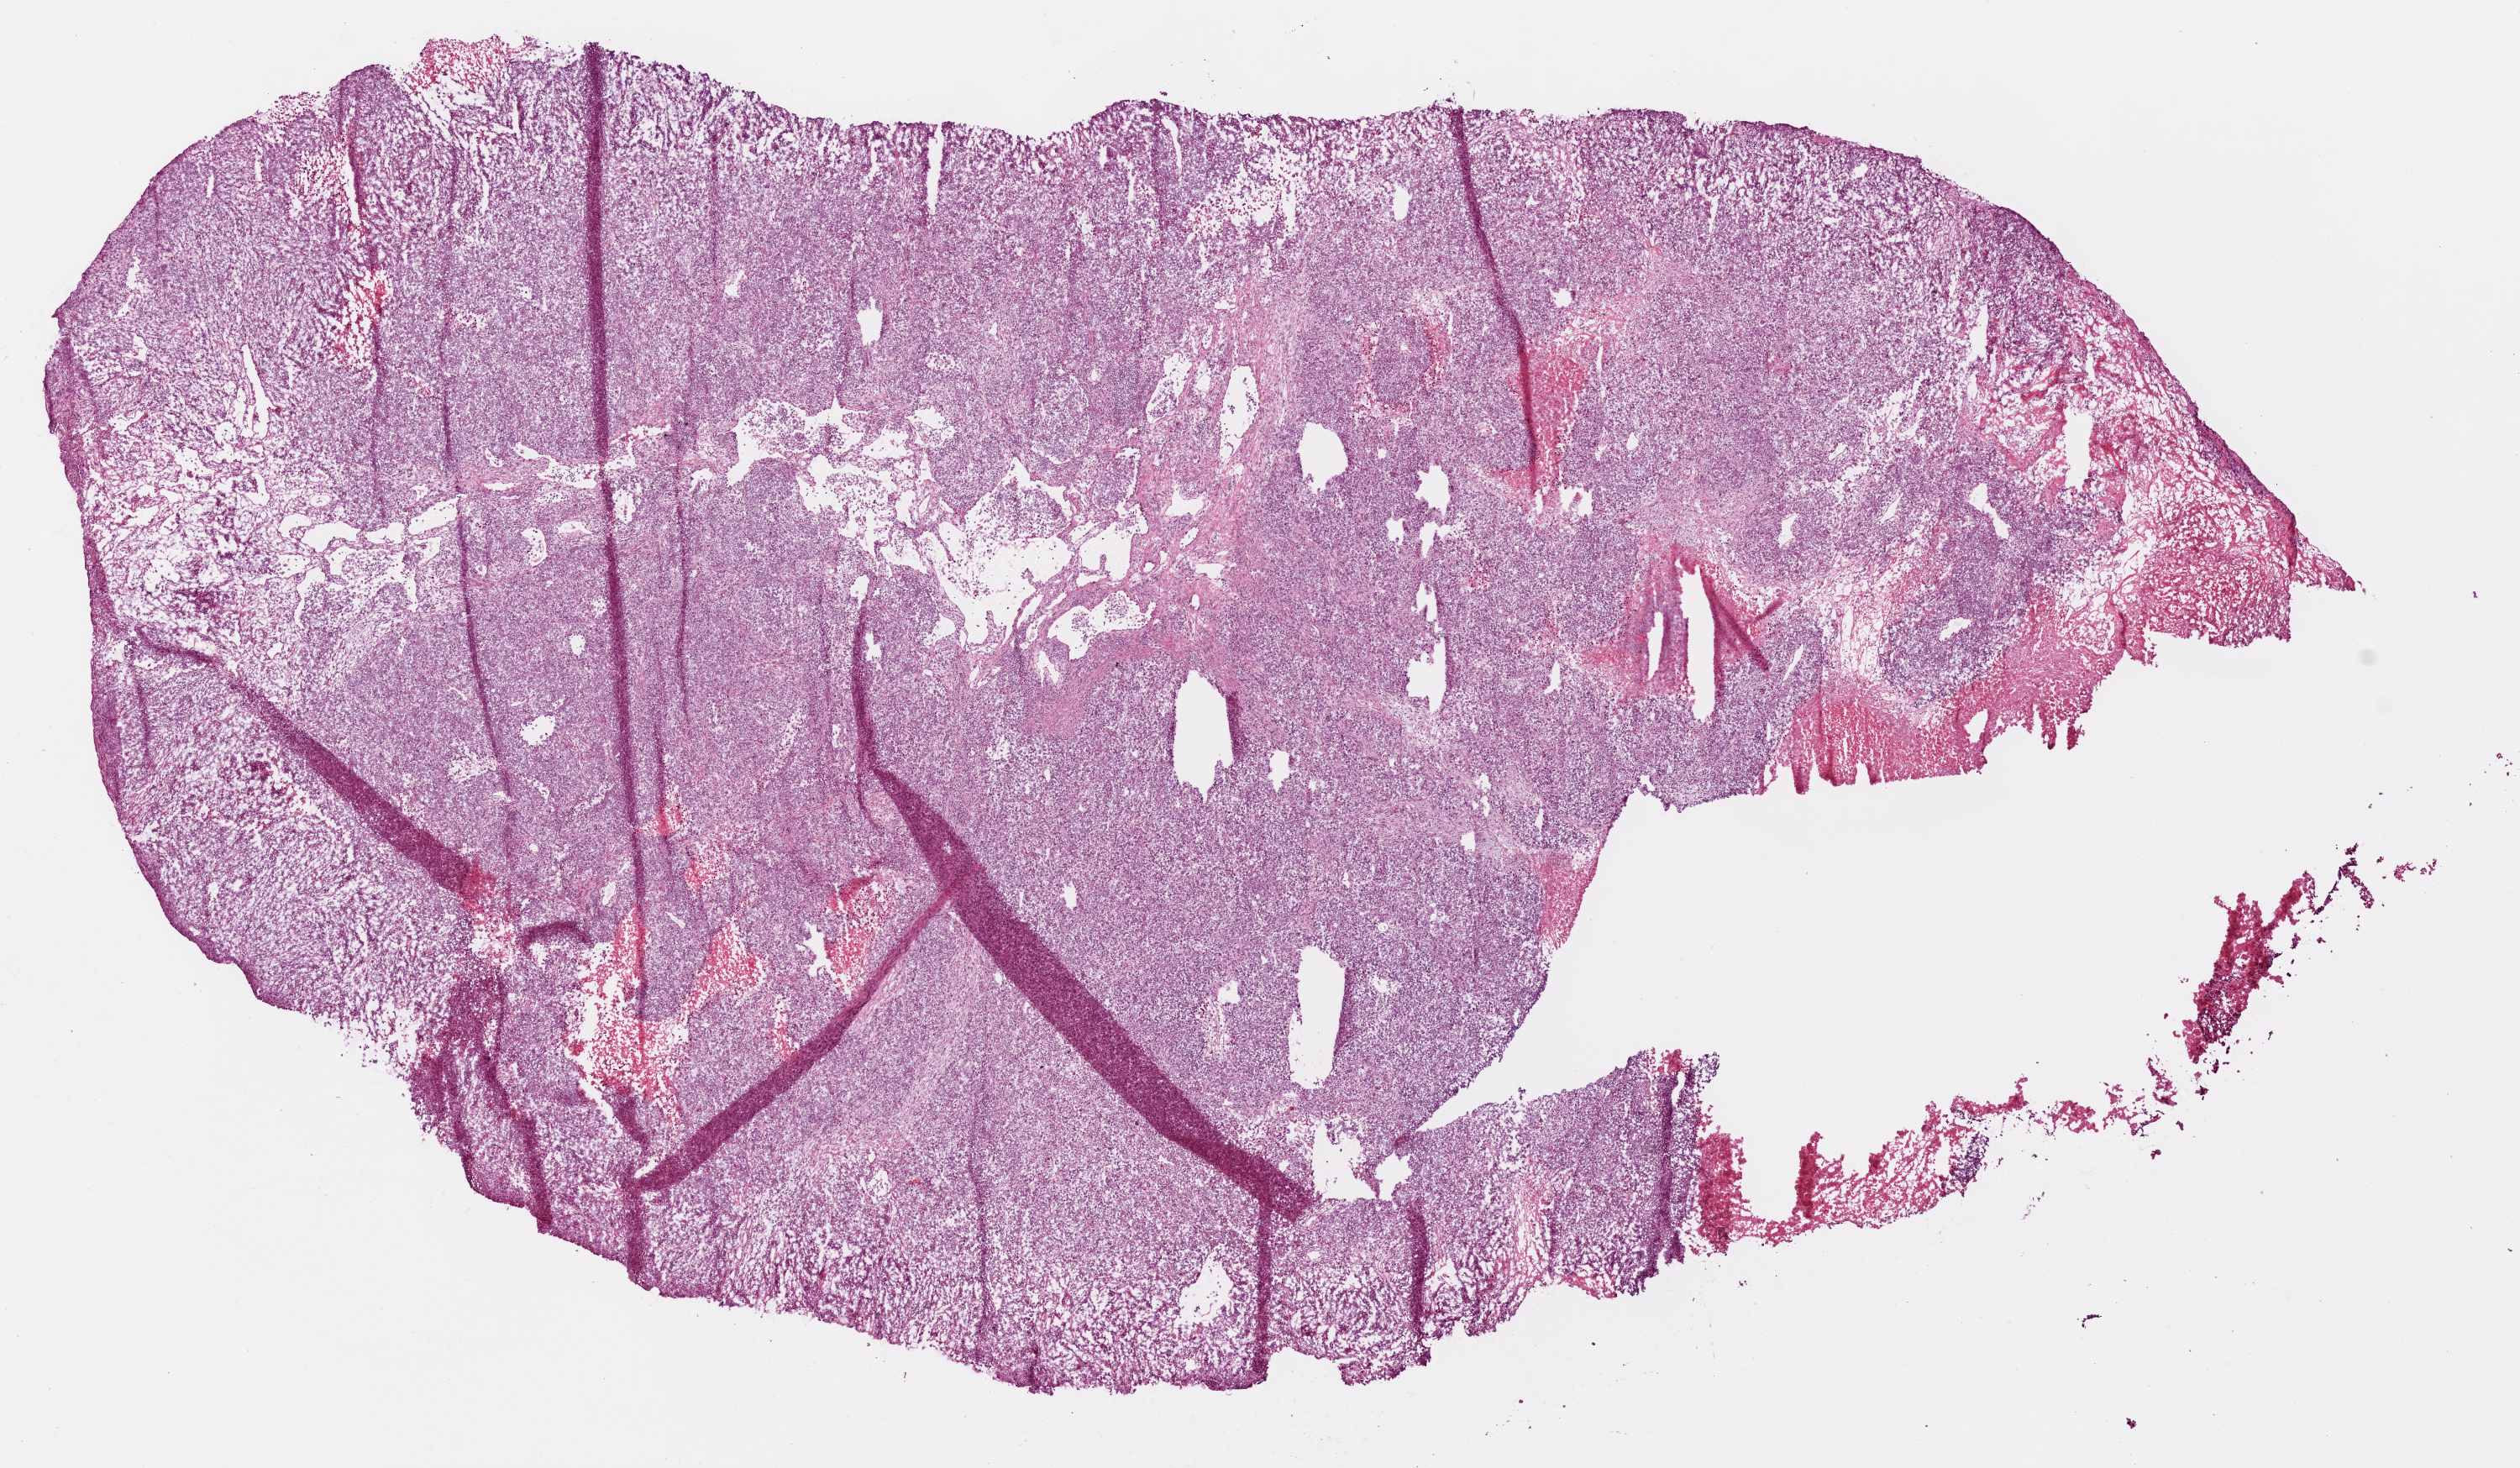
Whole-slide histology image, H&E, shown as a low-resolution overview of the whole scanned area (about 12.0 x 7.0 mm). Frozen section. Lung, primary tumour sample. Female patient; age at initial diagnosis 65 years. Composition of this section per pathologist review: tumour cells 79%, tumour nuclei 75%, normal cells 8%, stromal cells 5%, necrosis 8%.
Pathologic diagnosis: Squamous cell carcinoma, NOS (upper lobe, lung). AJCC pathologic stage: IA (7th edition).